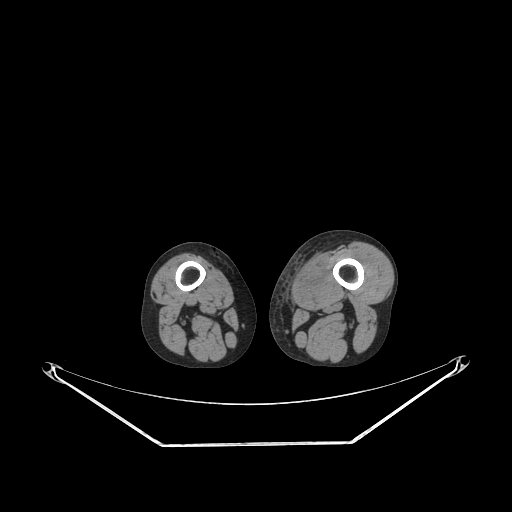
CT of an extremity soft-tissue mass (from a PET/CT study), one axial slice; position 207 of 267 along the scan axis; soft-tissue window (W 400 / L 40 HU); 3.75 mm slice thickness; 512 × 512 image matrix. Male patient. From the clinical record (not read from this slice): histological type: pleiomorphic leiomyosarcoma; grade: high; site of the primary tumour: left thigh.
Outlined on this slice (expert contour drawn on MRI and transferred to this co-registered scan by the dataset authors):
- gross tumour volume including surrounding oedema: bounding box [x1, y1, x2, y2] px = [294, 253, 328, 305]